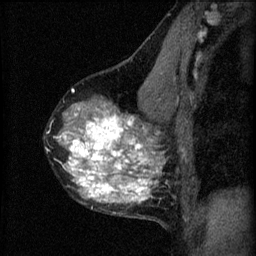
Breast MRI (dynamic contrast-enhanced), one sagittal slice; 3 images stored at this slice position (order not interpretable as contrast timing); 1.5 T; TE 4.2 ms, TR 8.2 ms; 2 mm slice thickness; 256 × 256 image matrix, field of view 180 × 180 mm. Female patient, age 40 years.
Structures marked on this image (semi-automatic segmentation, software-assisted and operator-edited):
- analysis volume of interest (the breast-tissue region the enhancement analysis was run in; not a lesion): box from (x=44, y=76) to (x=179, y=219) px
- tumour enhancement mask (voxels above the 70 % enhancement threshold inside the analysis volume of interest): (x=56, y=114)–(x=165, y=203)